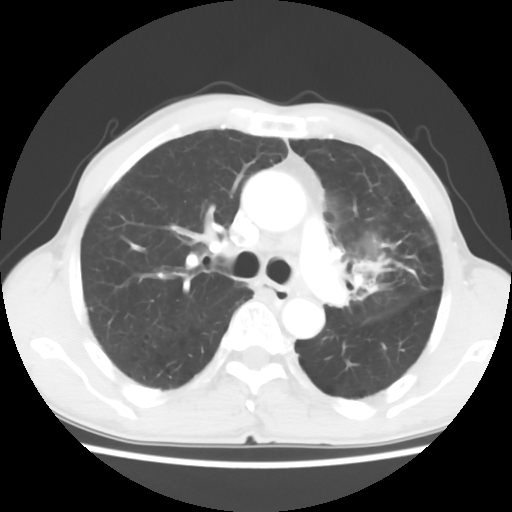
Chest CT, one axial slice. Slice 38 of 60 in the series (ordered by position). Lung window (W 1500 / L -600 HU). 512 × 512 image matrix, field of view 308 × 308 mm. Male patient, age 64 years. Case-level facts recorded for this patient, not image findings: clinical TNM (as recorded): T3 N3 M0.
Annotated regions visible in this slice (bounding box drawn by a radiologist):
- lung tumour (recorded histology: adenocarcinoma): bounding box <339,232,397,315> (left, top, right, bottom; pixels)